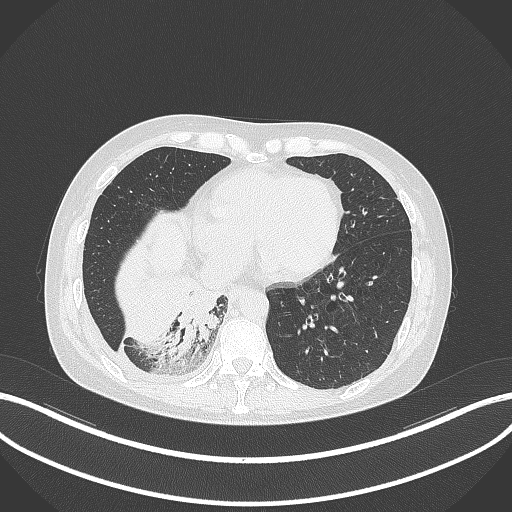
Chest CT, one axial slice; slice 92 of 329 in the series (ordered by position); lung window (W 1500 / L -600 HU); 1 mm slice thickness; 512 × 512 image matrix, field of view 400 × 400 mm. Patient: female, 63 years. From the clinical record (not read from this slice): clinical TNM (as recorded): T1c N0 M0.
Structures marked on this image (bounding box drawn by a radiologist):
- lung tumour (recorded histology: adenocarcinoma): box from (x=168, y=275) to (x=219, y=358) px